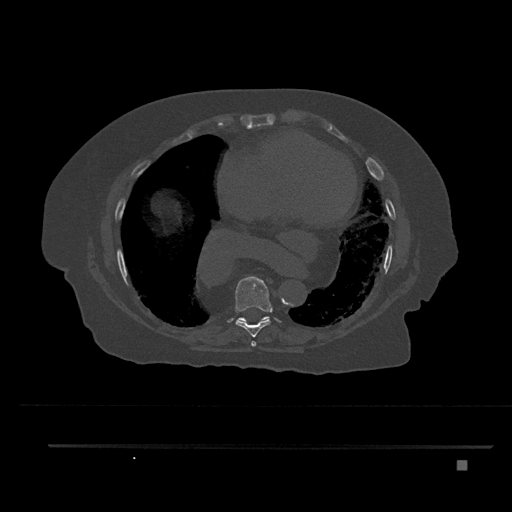
CT including the spine, one axial slice; slice 433 of 797 in the series (ordered by position); 120 kVp; bone window (W 1800 / L 400 HU); 0.5 mm slice thickness; 512 × 512 image matrix, field of view 437 × 437 mm. Female patient, age 76 years. From the clinical record (not read from this slice): primary cancer: lung; vertebrae with lytic lesions (as recorded): T11, L3.
Structures marked on this image (semi-automatically segmented with operator editing):
- T7 vertebra: box from (x=251, y=341) to (x=256, y=347) px
- T8 vertebra: (x=235, y=276)–(x=271, y=347)
- T9 vertebra: (x=238, y=316)–(x=269, y=323)